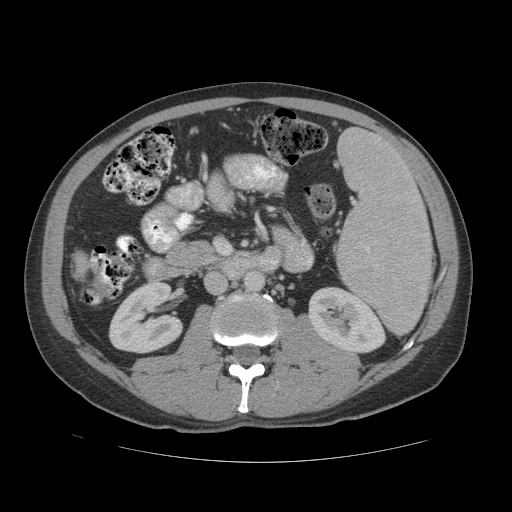
Contrast-enhanced abdominal CT (liver protocol), one axial slice; reconstruction kernel STANDARD; soft-tissue window (W 400 / L 40 HU); 2.5 mm slice thickness; 512 × 512 image matrix. From the clinical record (not read from this slice): diagnosis: hepatocellular carcinoma (patient treated with transarterial chemoembolisation; whether this scan precedes or follows treatment is not stated here); TNM stage (as recorded): Stage-IVB; Child-Pugh class: B; tumour differentiation: well differentiated; tumour nodularity: multinodular.
Outlined on this slice (semi-automatic segmentation, software-assisted and operator-edited):
- liver parenchyma outside the tumour (the mass and vessels are separate outlines, so this box may not span the whole liver): bounding box [x1, y1, x2, y2] px = [74, 256, 82, 268]